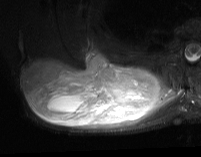
MRI of an extremity soft-tissue mass, one axial slice; slice 32 of 74 in the series (ordered by position); STIR; MR volume resampled by the dataset authors to the PET/CT grid (not the native acquisition matrix); 3.27 mm slice thickness; 201 × 157 image matrix. Male patient. From the clinical record (not read from this slice): histological type: pleiomorphic spindle cell undifferentiated; grade: high; site of the primary tumour: right parascapusular.
Annotated regions visible in this slice (expert contour drawn on MRI and transferred to this co-registered scan by the dataset authors):
- gross tumour volume including surrounding oedema: box from (x=23, y=54) to (x=178, y=129) px
- gross tumour volume (mass): (x=23, y=54)–(x=162, y=127)